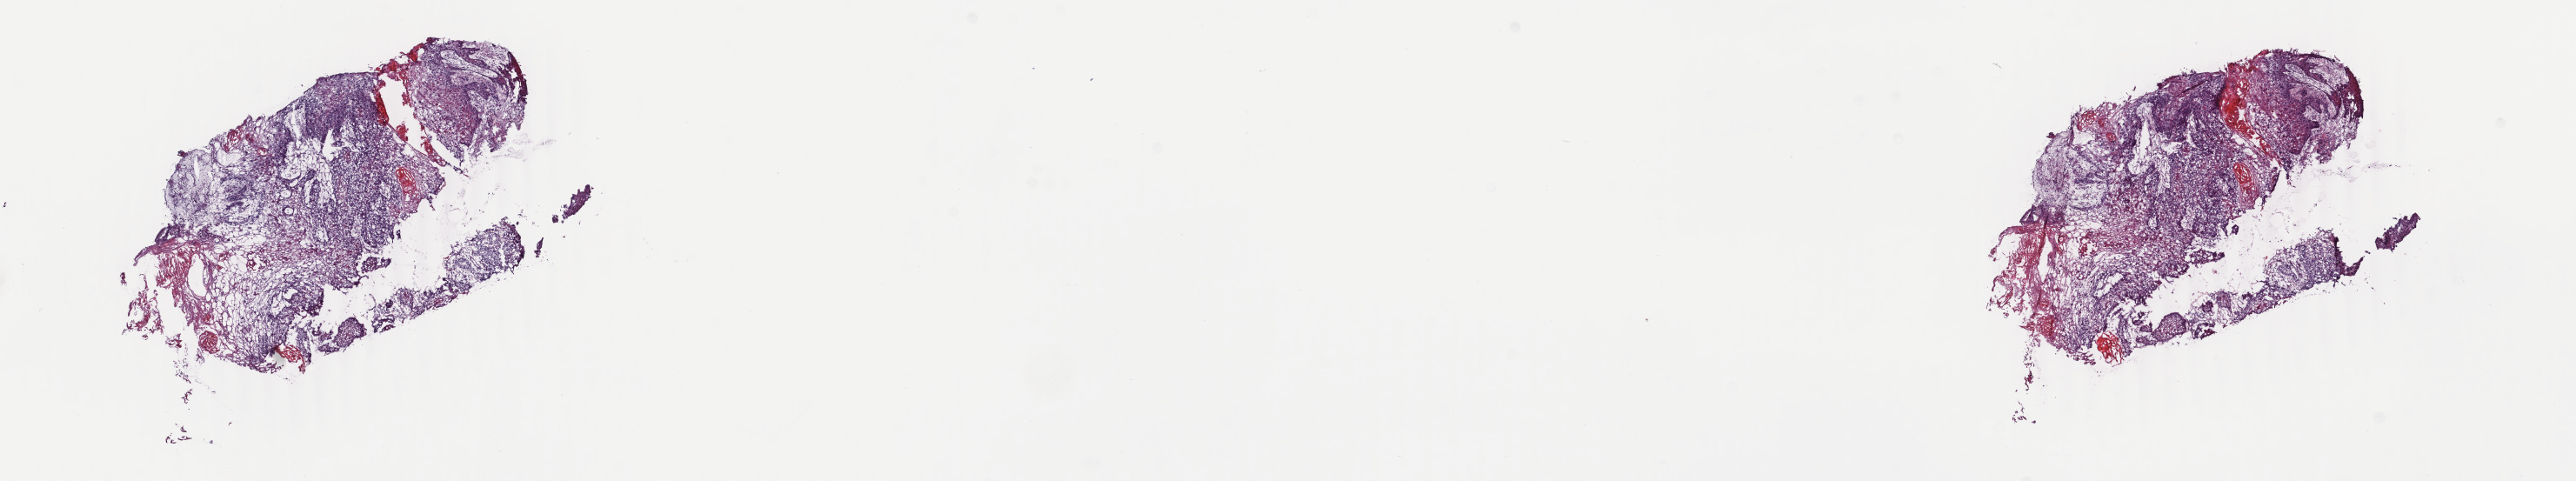
Digitized H&E-stained tissue section (whole slide) — whole scanned area (about 23.6 x 4.4 mm) shown as a low-resolution overview, frozen section from the top of the tissue portion, sample: primary tumour, head and neck. Patient: male, age at initial diagnosis 58 years. Histologic grade: G2 (moderately differentiated). Slide review estimates, as recorded: tumour cells 45%, tumour nuclei 80%, normal cells 0%, stromal cells 37%, necrosis 18%. Inflammatory infiltration, as recorded: lymphocyte infiltration 4%, monocyte infiltration 1%, neutrophil infiltration 1%.
TNM: T2 N0 M0. AJCC pathologic stage: II (7th edition). Laterality: midline. Histologic diagnosis: Squamous cell carcinoma, NOS (border of tongue).